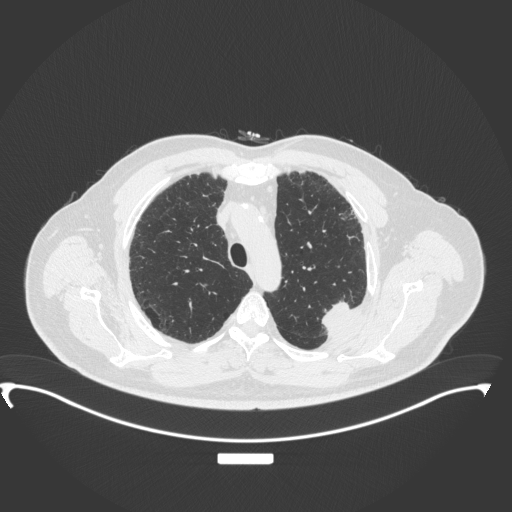
Chest CT, one axial slice; slice 279 of 350 in the series (ordered by position); reconstruction kernel B31f; lung window (W 1500 / L -600 HU); 512 × 512 image matrix, field of view 459 × 459 mm. Male patient, age 64 years. Case-level facts recorded for this patient, not image findings: clinical TNM (as recorded): T1c N1 M1.
Structures marked on this image (bounding box drawn by a radiologist):
- lung tumour (recorded histology: adenocarcinoma): bounding box (x1, y1, x2, y2) in pixels: (313, 295, 357, 334)